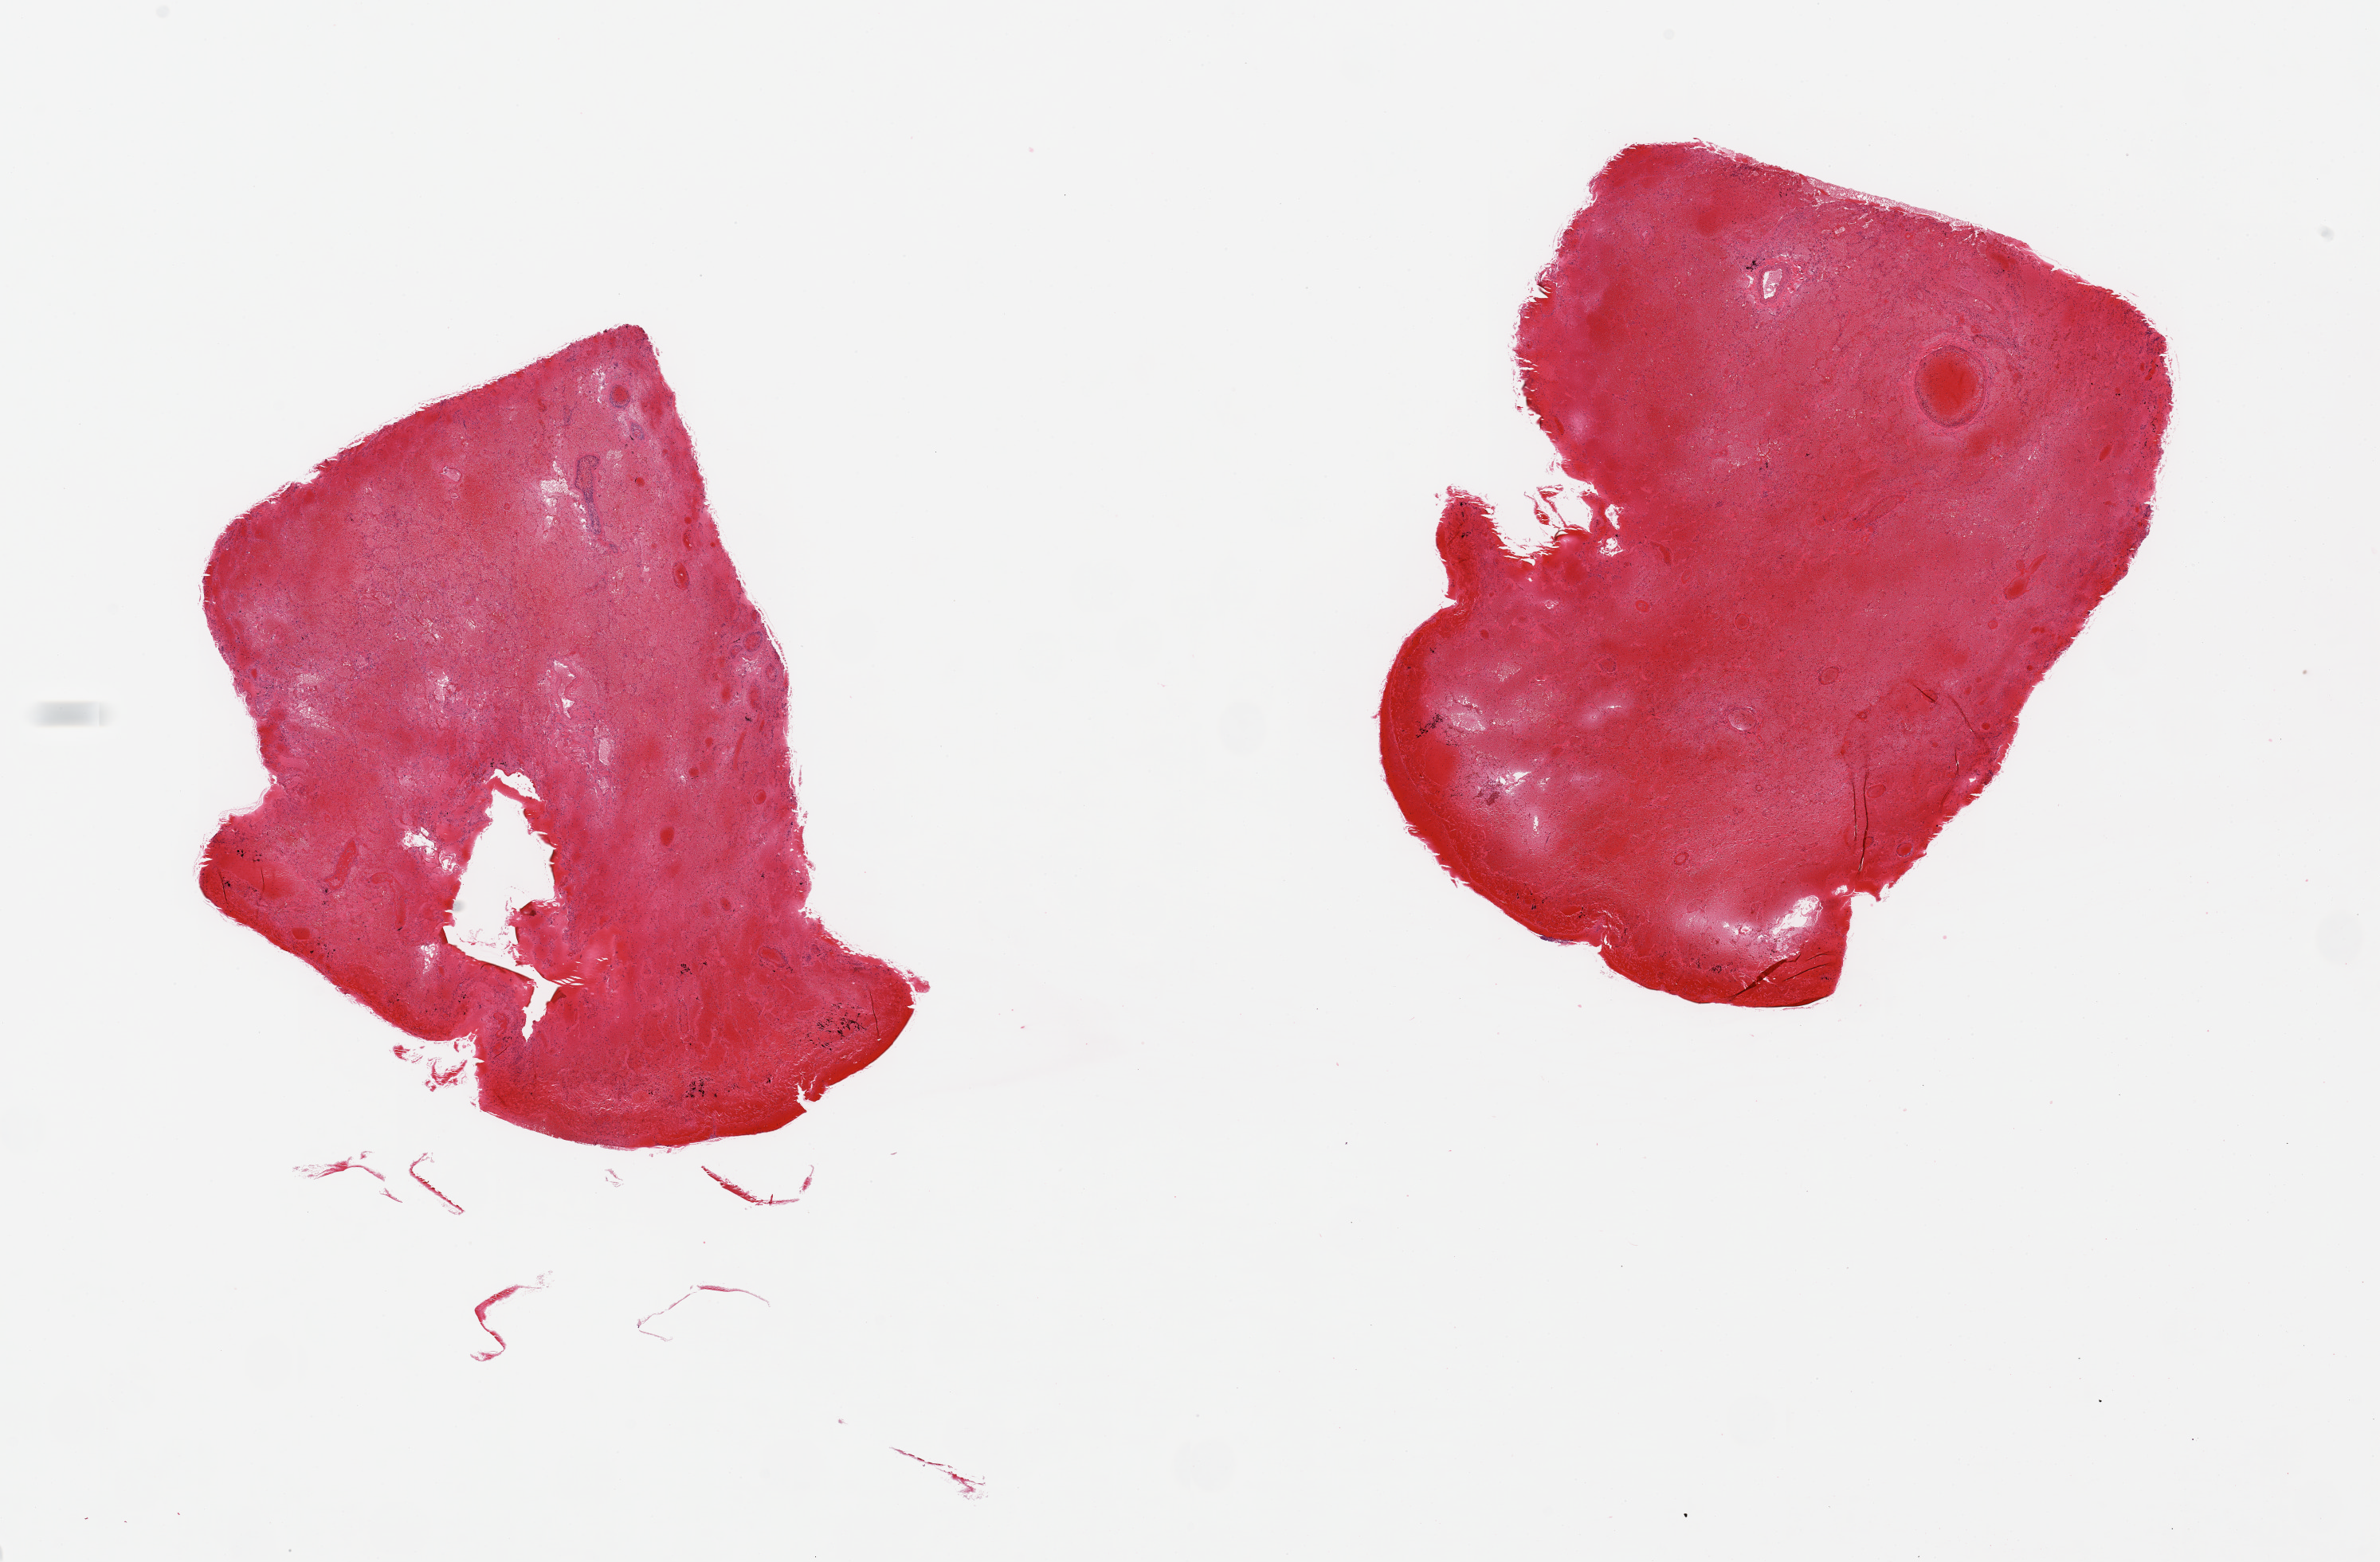
Hematoxylin and eosin (H&E) whole-slide image — shown as a low-resolution overview of the whole scanned area (about 23.6 x 15.5 mm, from a 20x scan); PAXgene-fixed, paraffin-embedded tissue; target tissue: lung; donor tissue sample. Donor sex: female.
Review note (as recorded): 2 pieces; completely hemorrhagic; tissue autolyzed; consistent with pulmonary embolism.